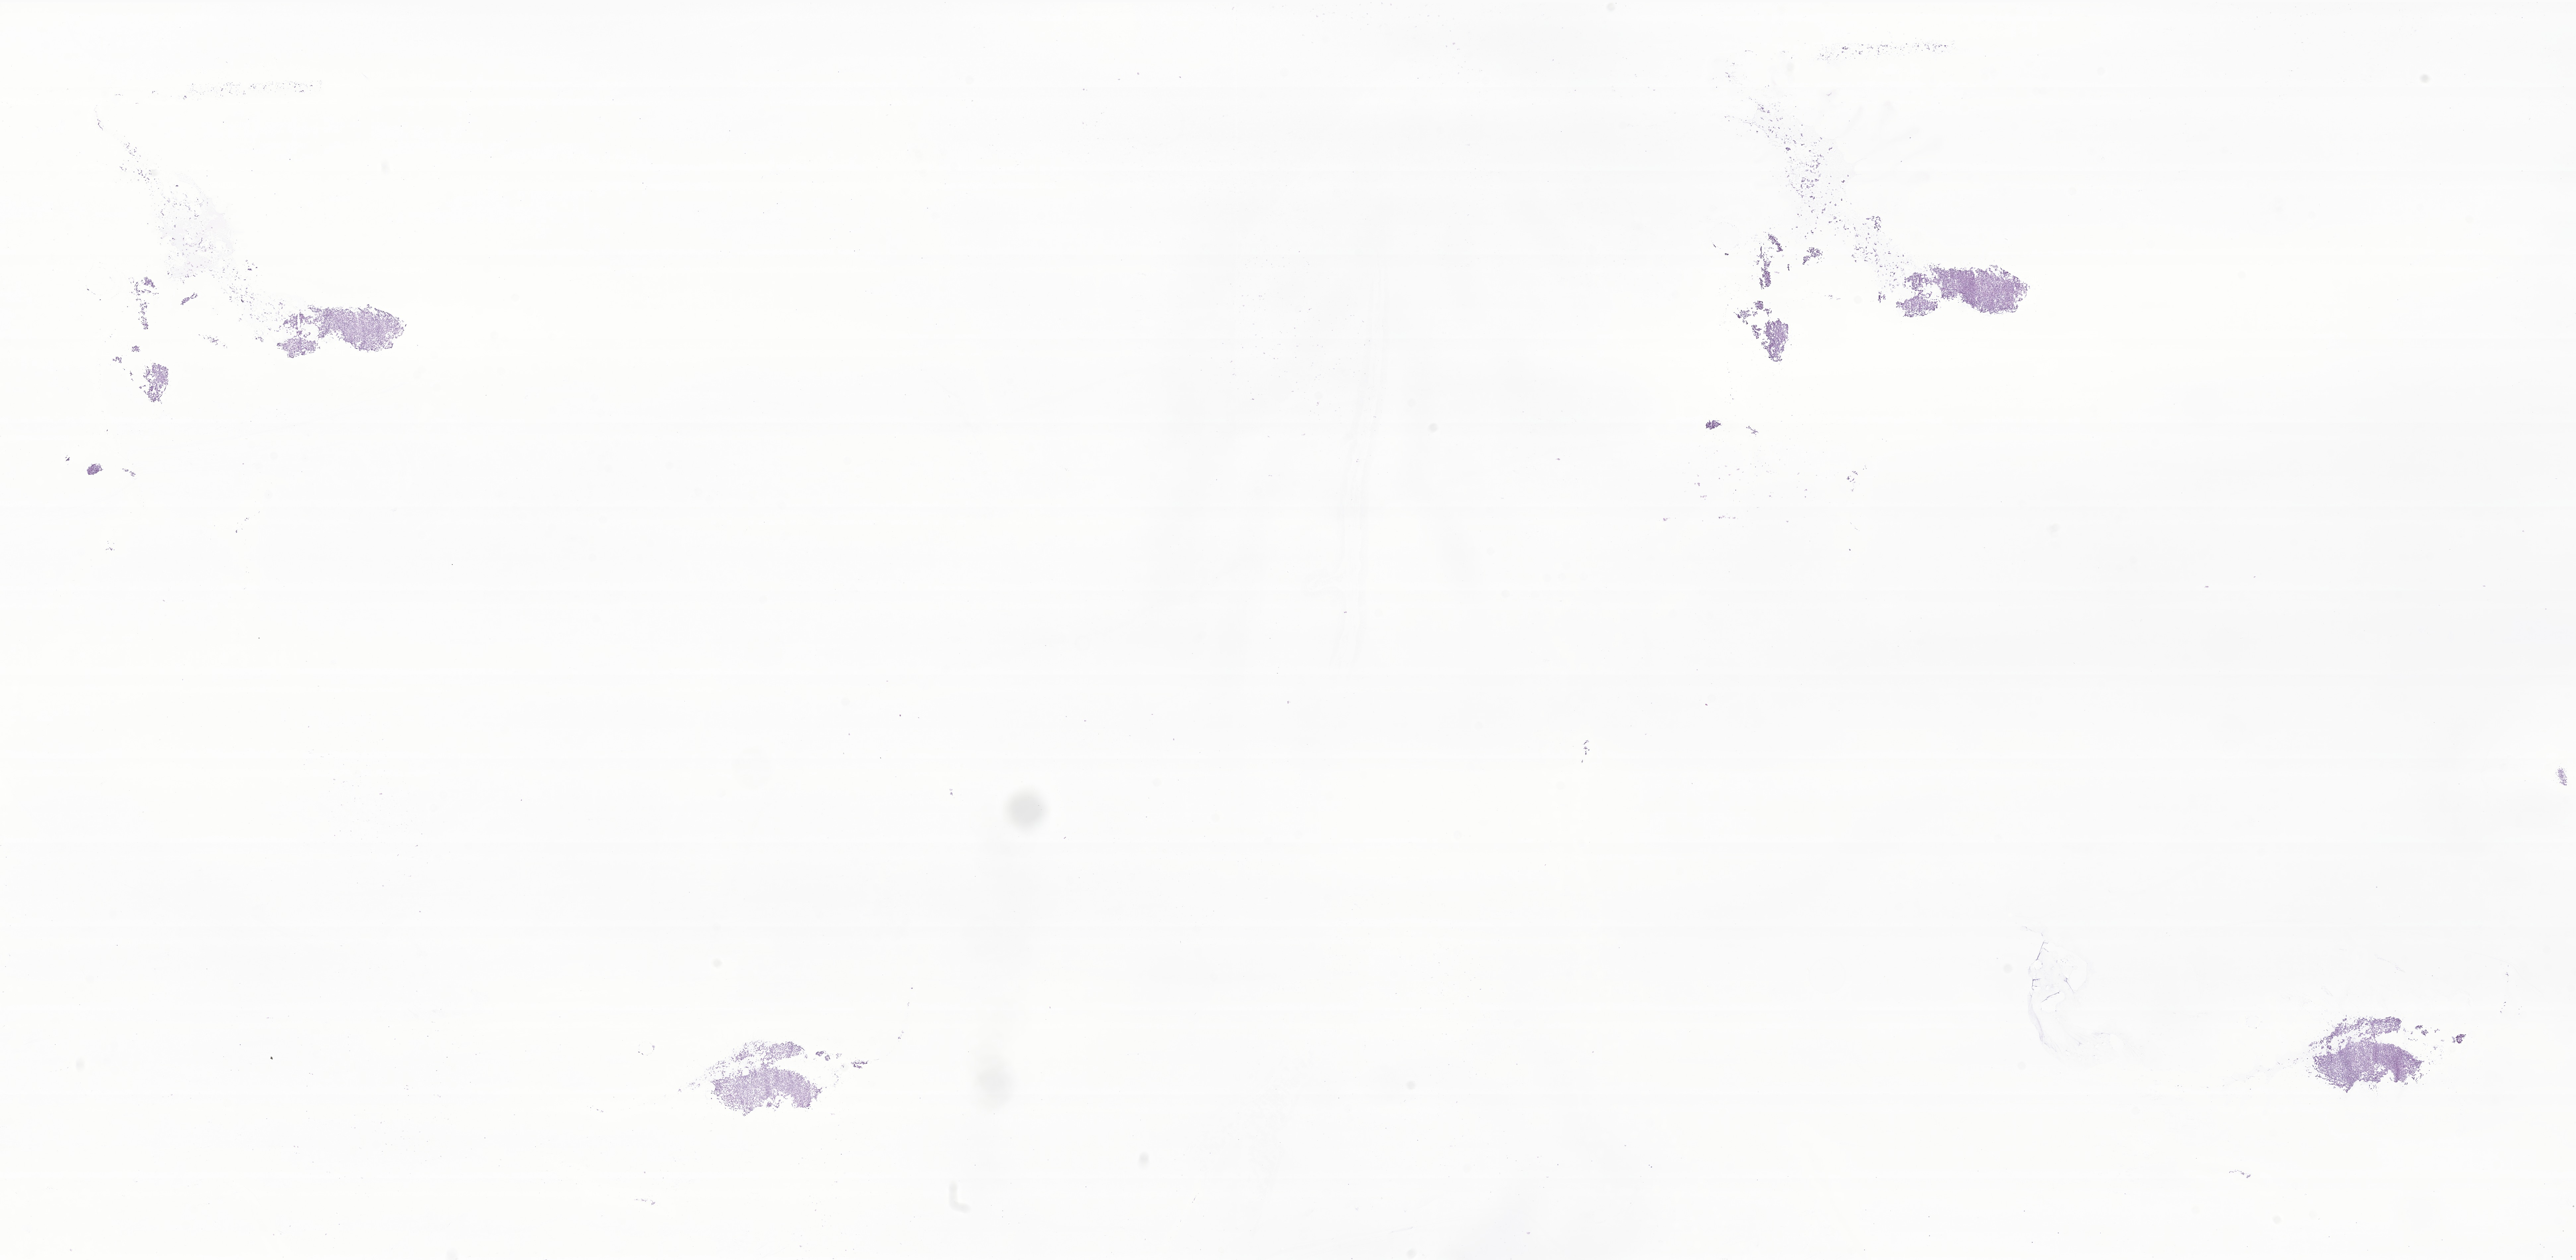
H&E whole-slide image of tumor tissue from the pelvis, low-resolution overview of the scanned area, about 32.7 x 16.0 mm; cryosection (OCT / tissue freezing medium). Patient: female, age 170 days.
Diagnosis (ICD-O-3 morphology term): Rhabdomyosarcoma, NOS.